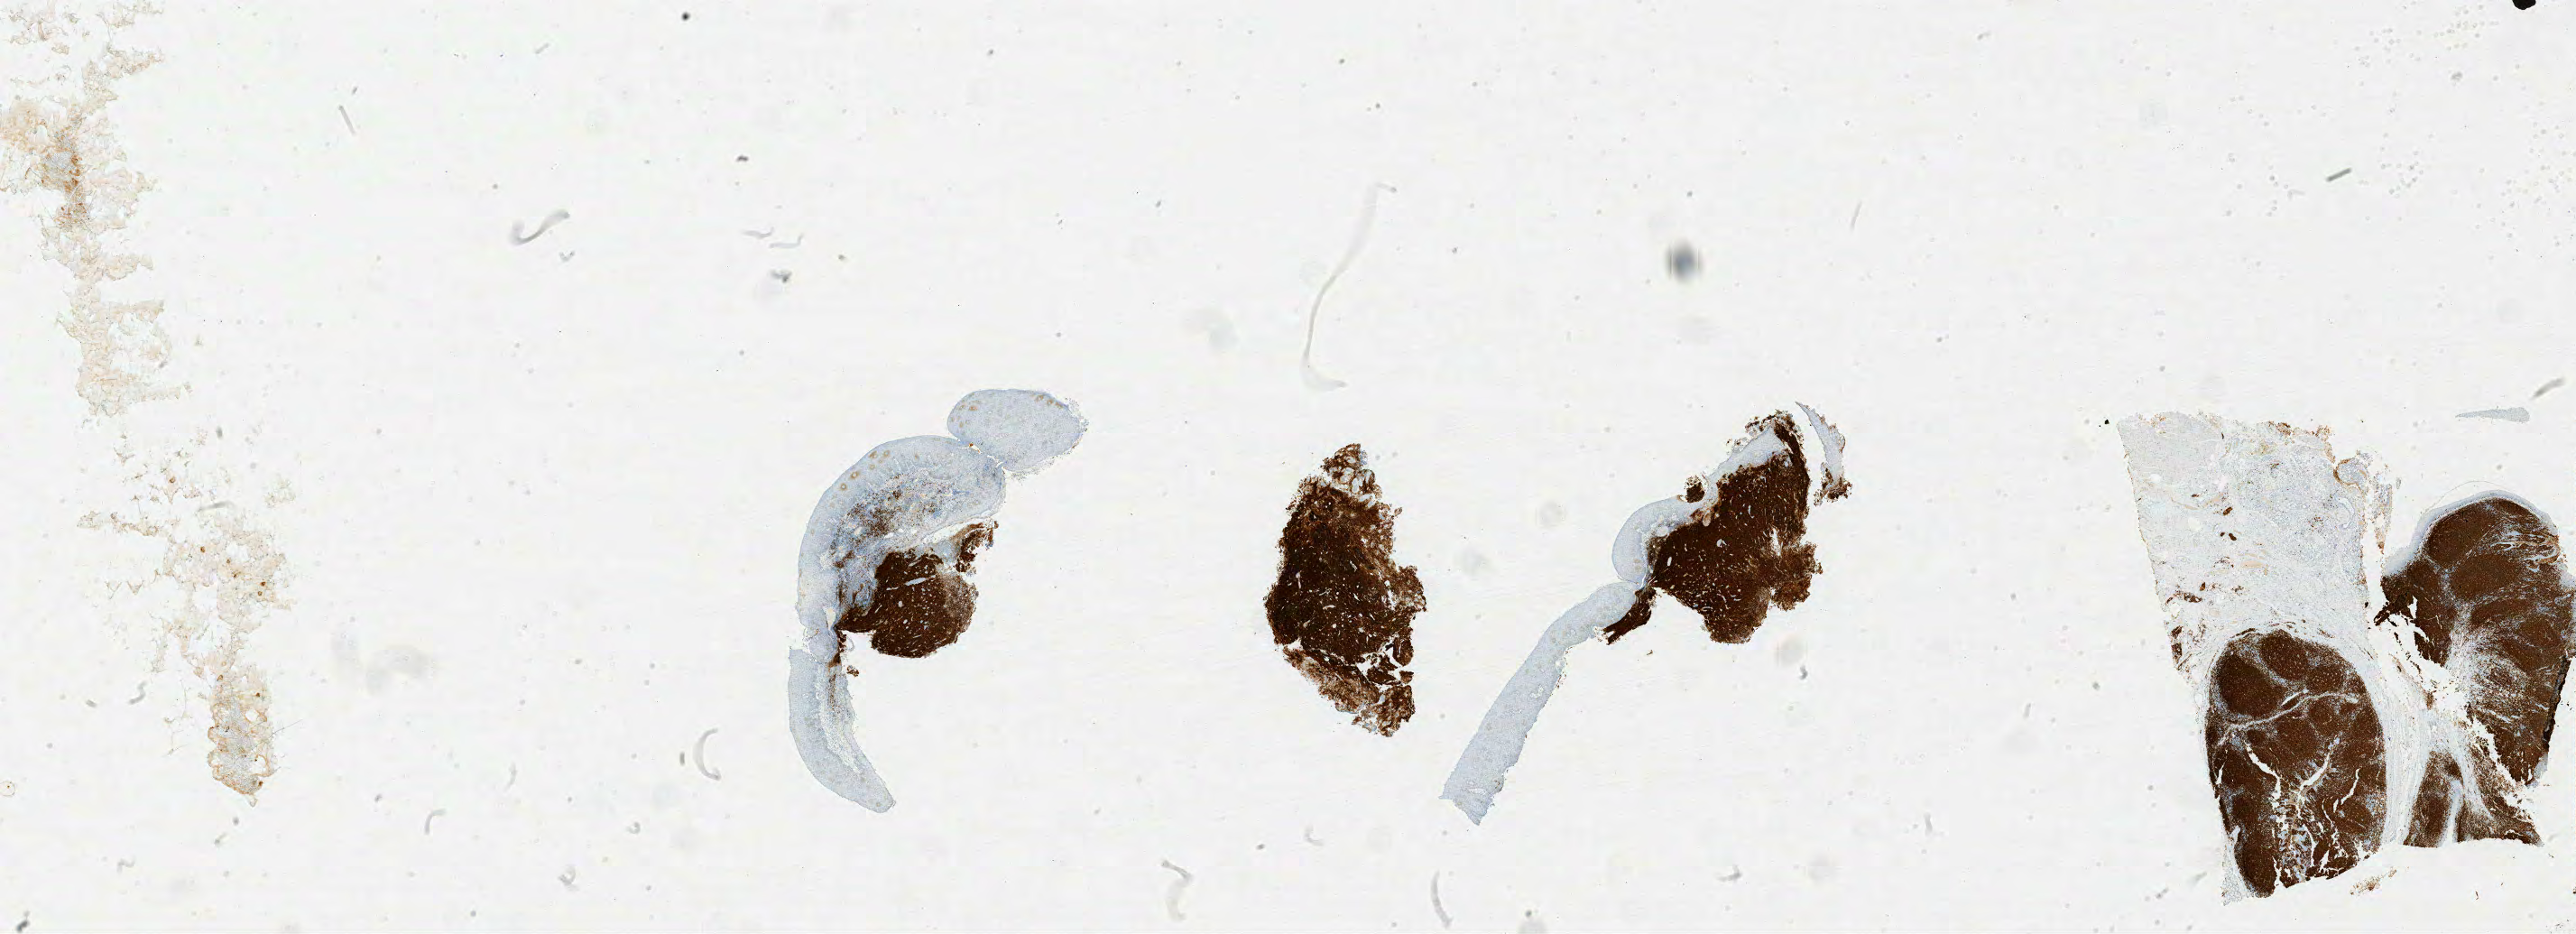
Whole-slide image, immunohistochemical stain for CD20, shown as a low-resolution overview of the whole scanned area (about 45.6 x 16.5 mm), tumor tissue. Patient male; 66 years old.
* diagnosis: Burkitt lymphoma, NOS